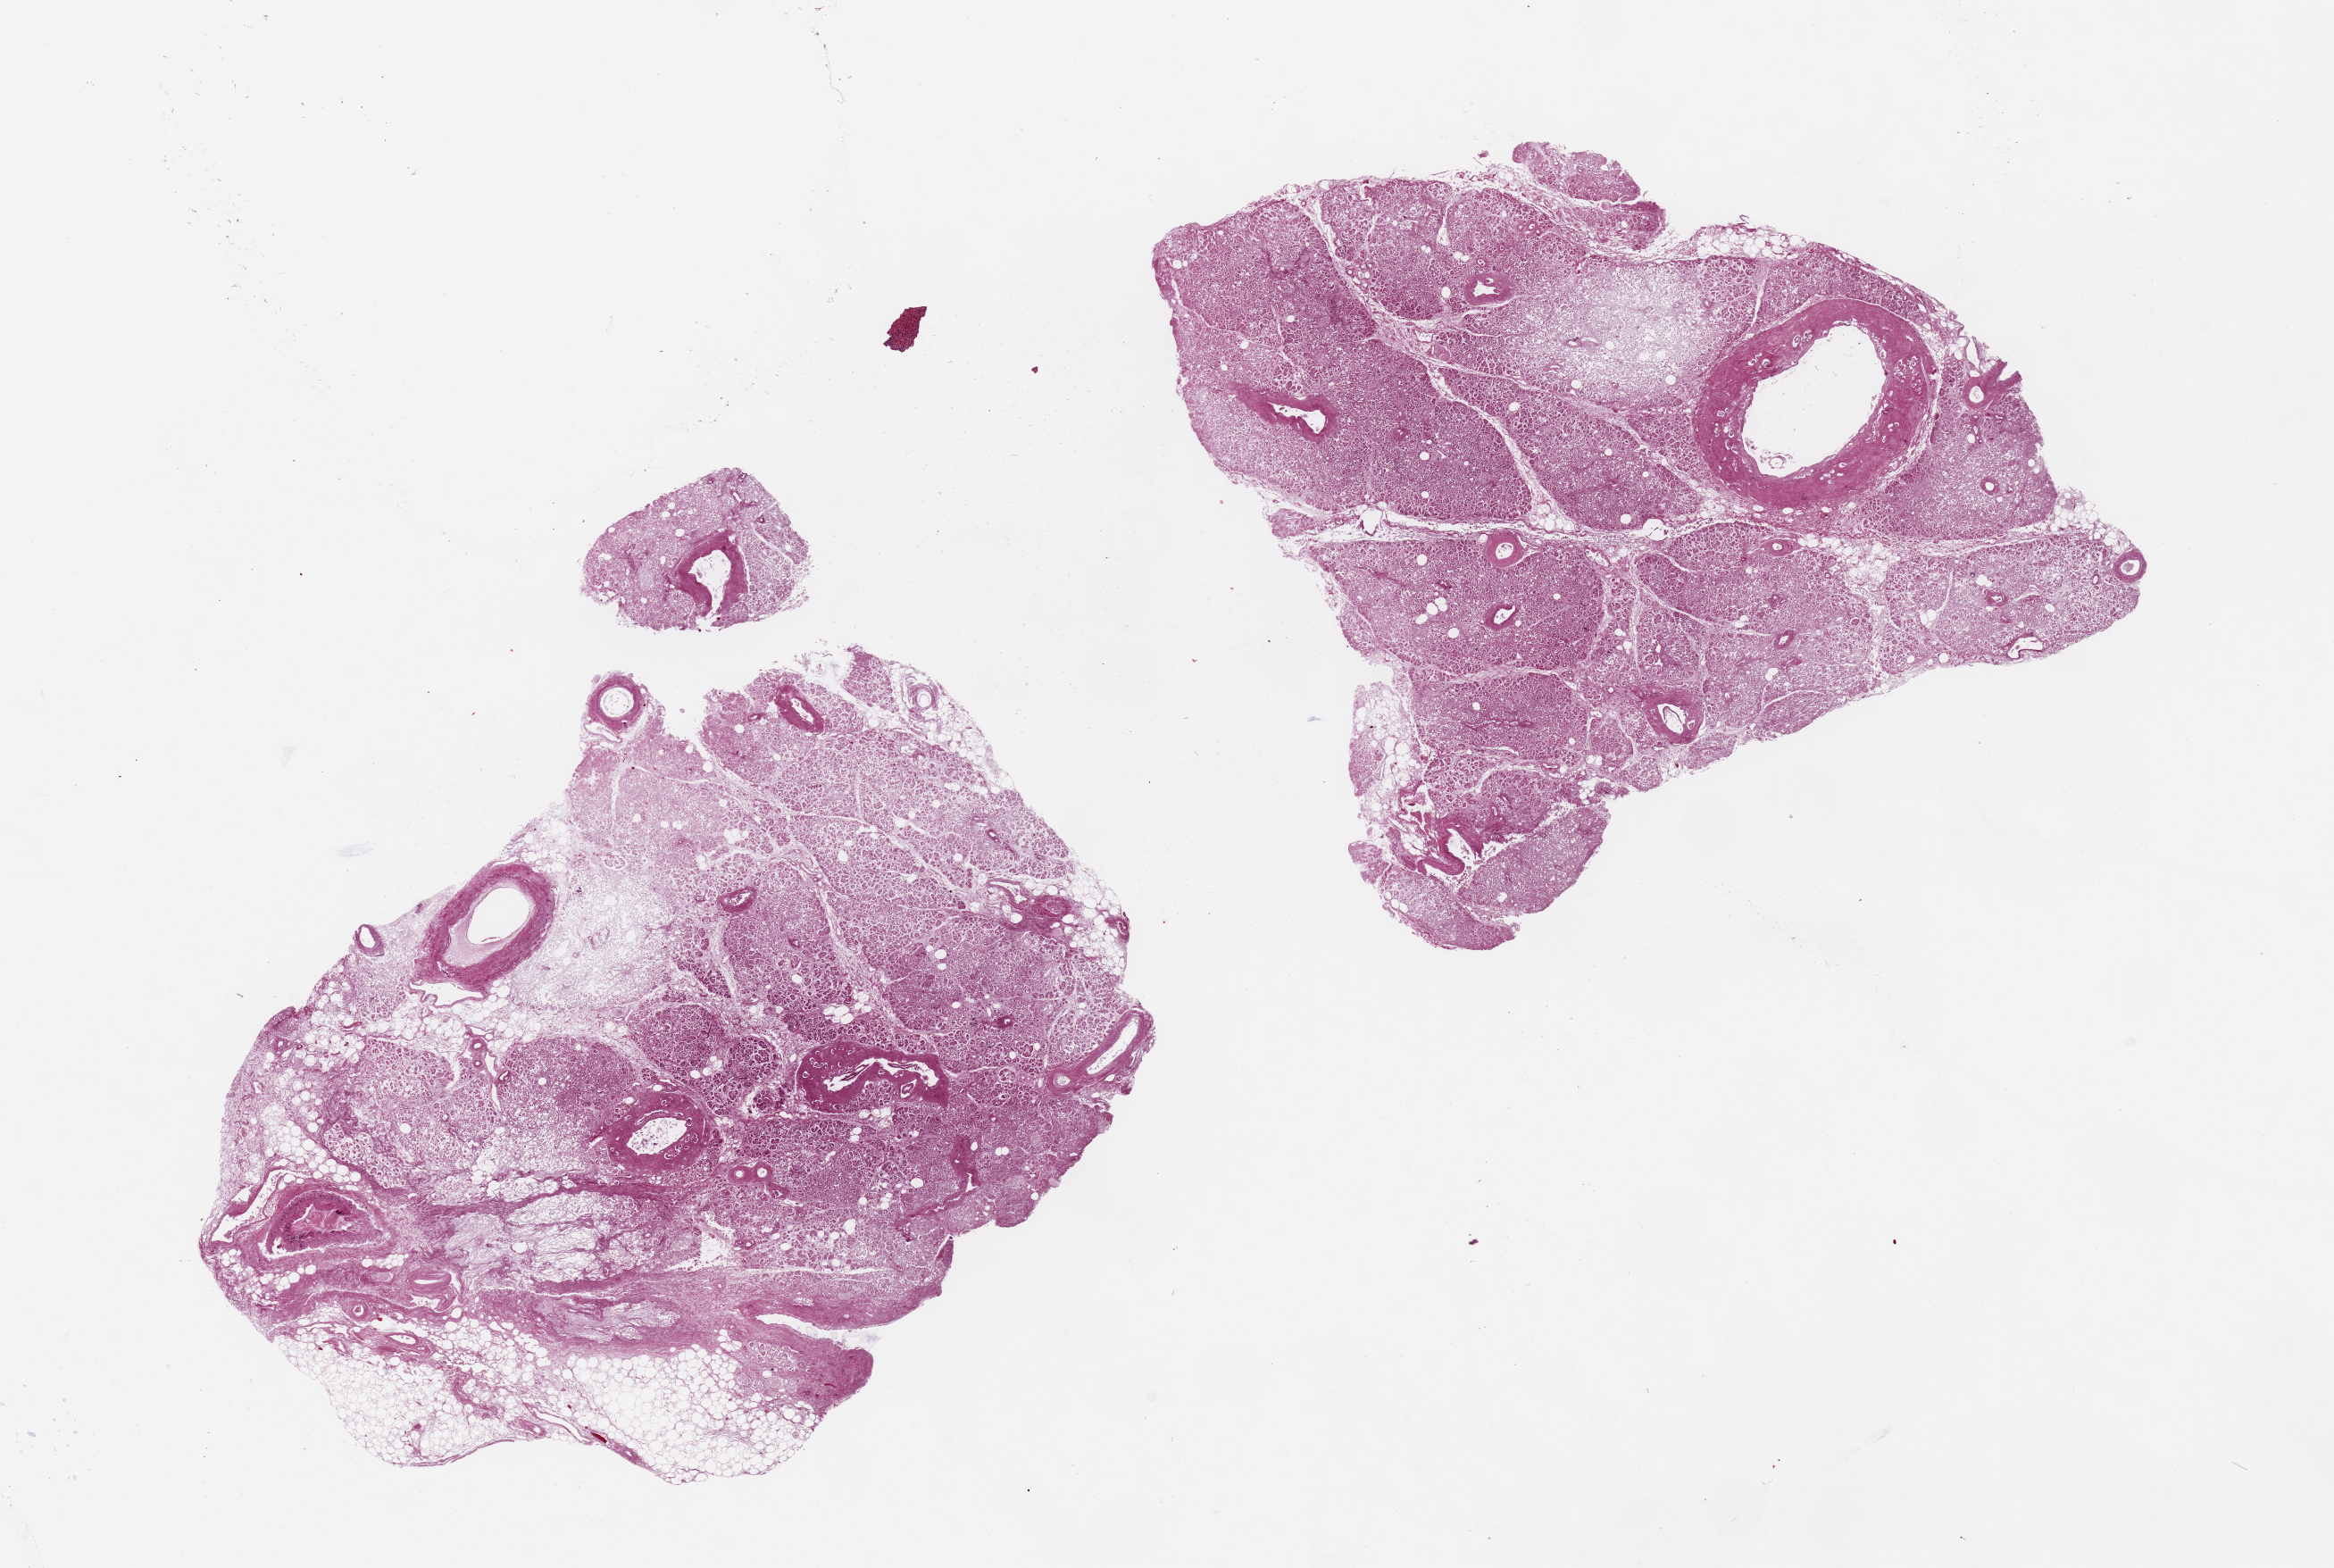
Digitized hematoxylin and eosin (H&E)-stained section — a low-resolution overview of the entire scanned area, about 20.7 x 13.9 mm, PAXgene-fixed paraffin-embedded (PFPE) section, target tissue: pancreas, tissue donor sample. Donor: female.
Reviewer comment on this tissue sample: 2 pieces 7x7 & 8x6 mm; severely autolyzed; 4x1 mm adipose at one edge.